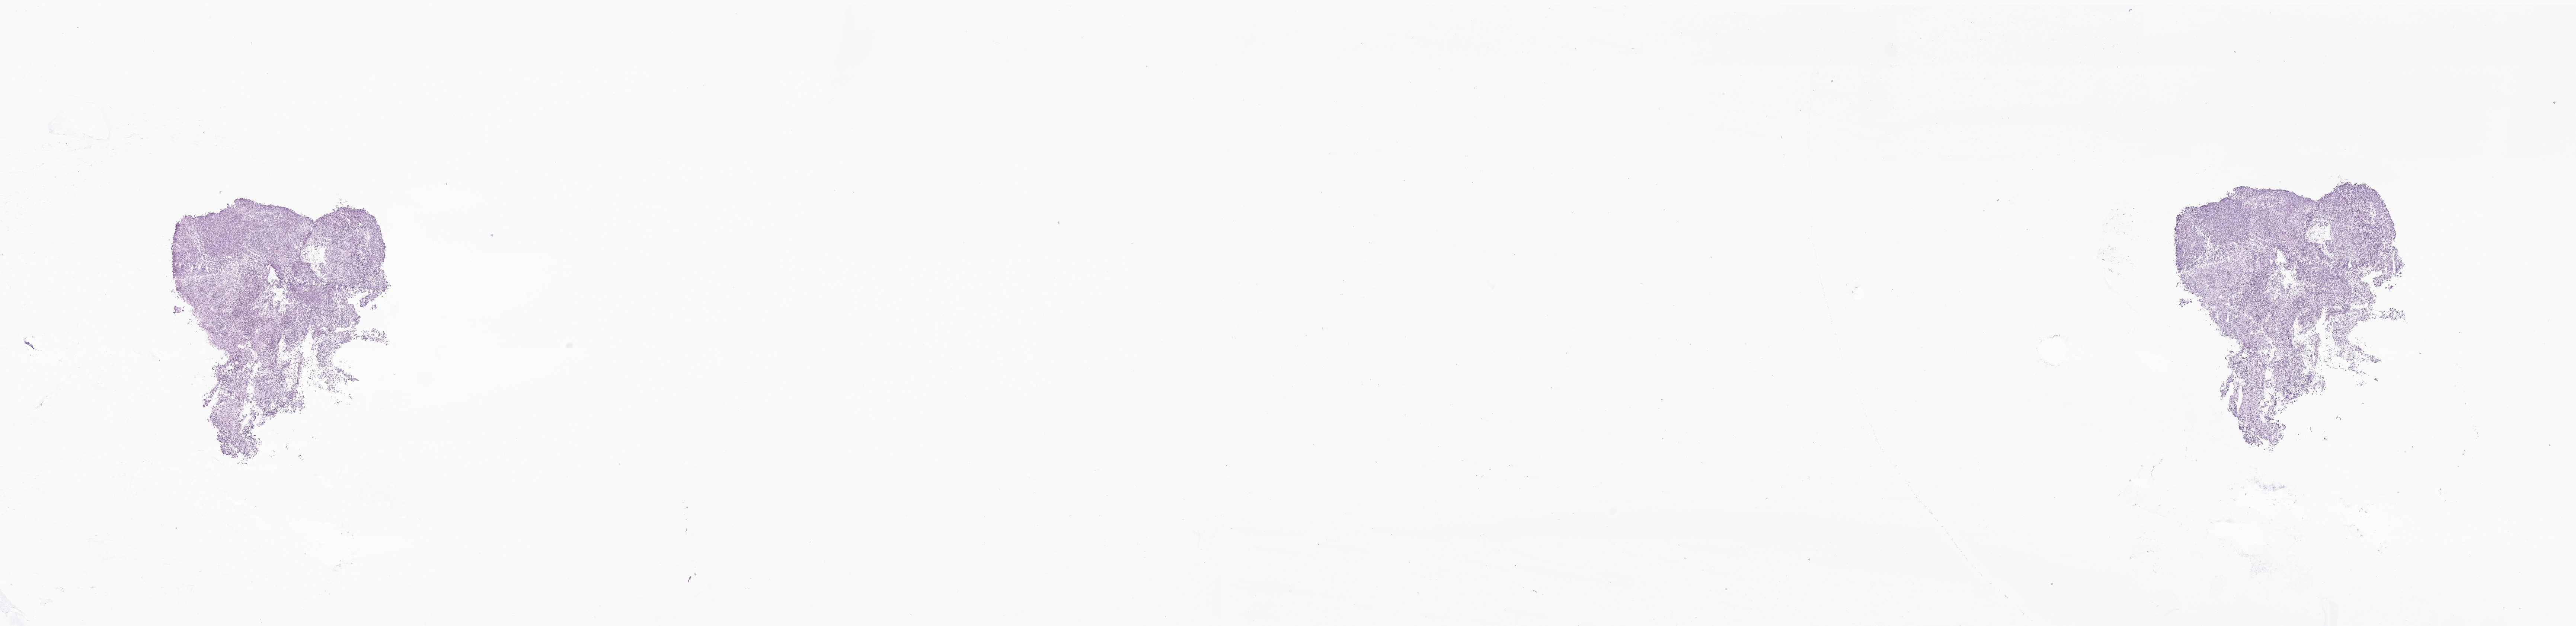
Whole-slide image, H&E stain of tumor tissue from the cerebellum, shown as a low-resolution overview of the whole scanned area (about 29.2 x 7.1 mm); frozen section. Patient: male, age 352 days.
Recorded diagnosis: Medulloblastoma, NOS.